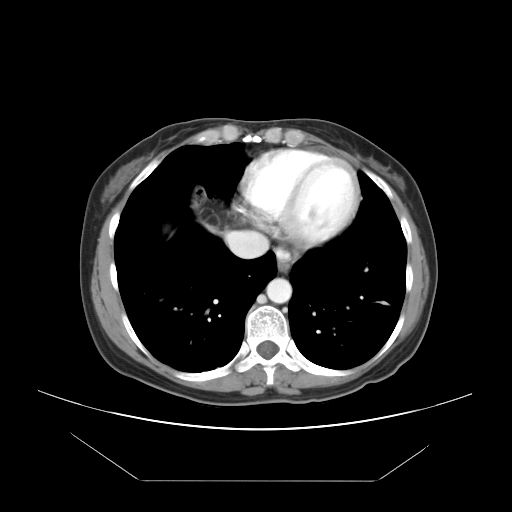
Contrast-enhanced abdominal CT, one axial slice; slice 43 of 45 in the series (ordered by position); 120 kVp; intravenous contrast given; soft-tissue window (W 400 / L 40 HU); 512 × 512 image matrix, field of view 405 × 405 mm. Female patient, age 52 years. Case-level facts recorded for this patient, not image findings: diagnosis: colorectal cancer liver metastases, imaged before liver resection; multiple liver metastases: yes; largest metastasis: 2.5 cm; disease in both lobes: no.
Structures marked on this image (expert manual segmentation):
- hepatic veins: box from (x=228, y=233) to (x=255, y=256) px